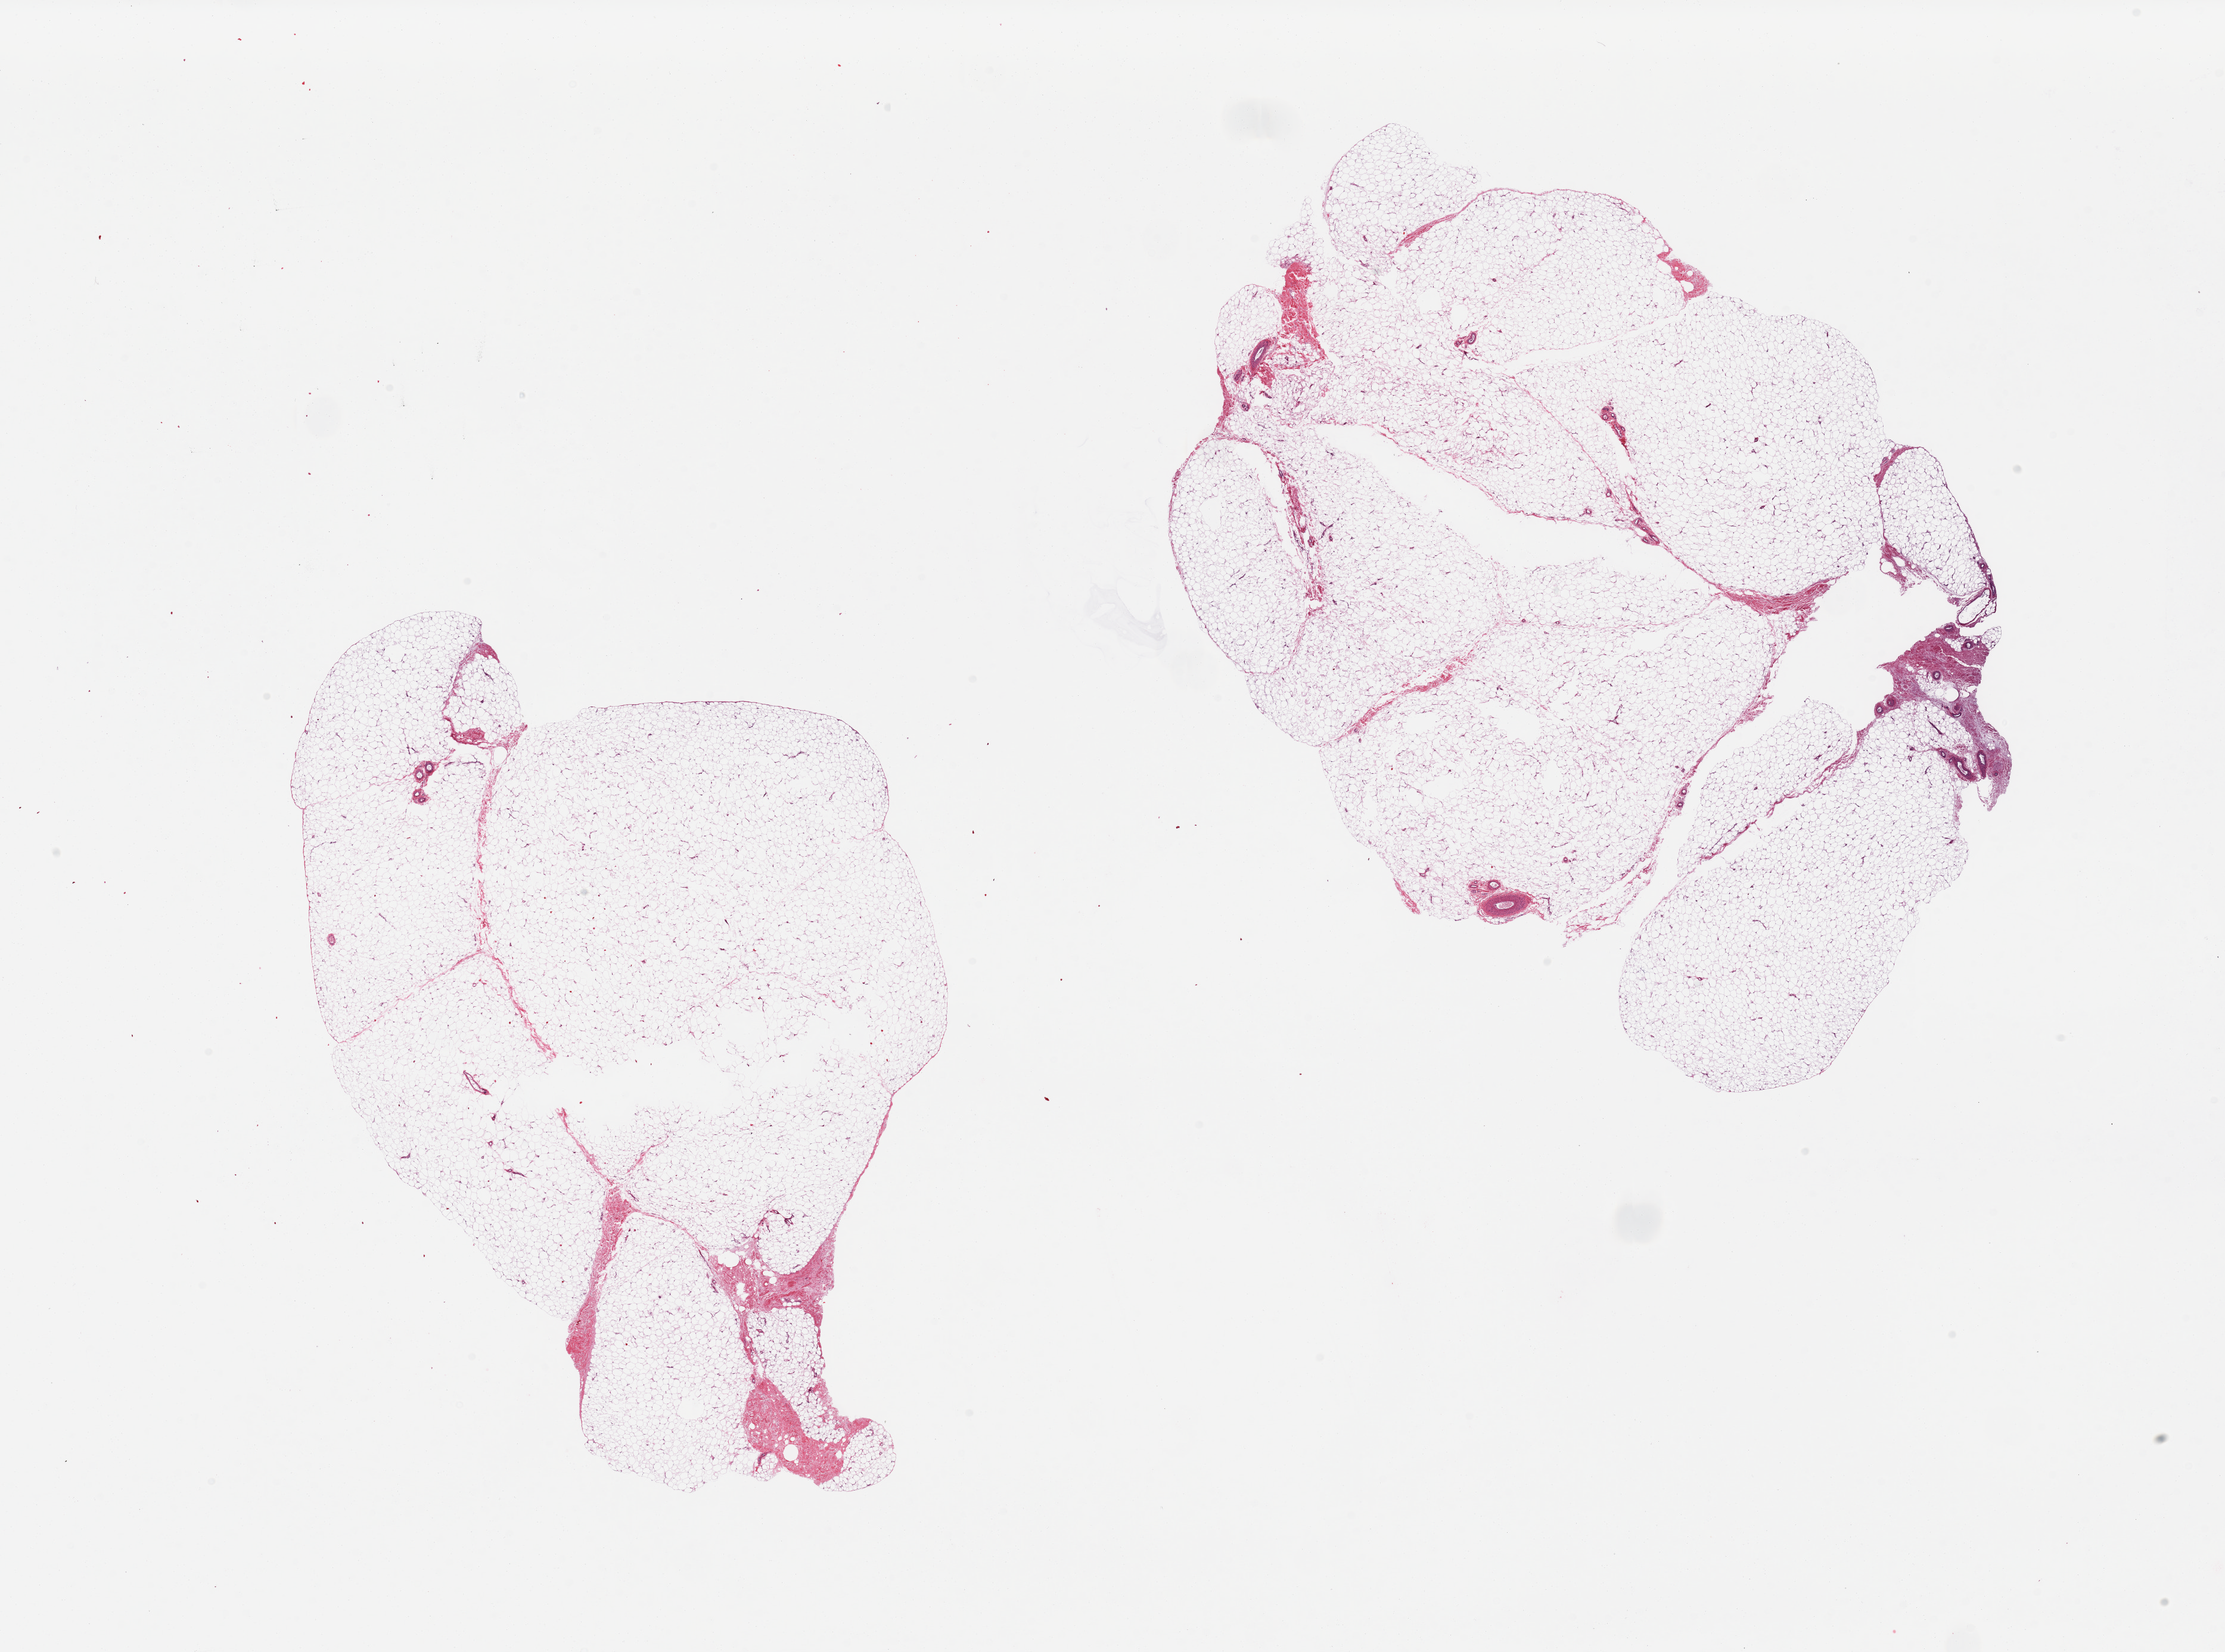
Digitized H&E-stained section, brightfield, low-resolution overview of the scanned area, about 29.5 x 21.9 mm (acquisition: 20x scan). PAXgene-fixed paraffin-embedded (PFPE) section. Section of adipose tissue (target tissue). Donor tissue sample. Male donor.
Pathologist's review note for this sample: 2 pieces, small component of fibrous tissue/vessels.